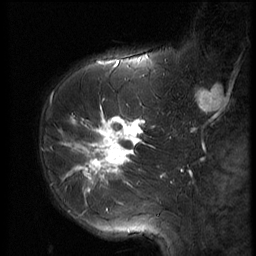
Breast MRI (dynamic contrast-enhanced), one sagittal slice; position 21 of 56 along the scan axis; 3 images stored at this slice position (order not interpretable as contrast timing); 1.5 T; TE 4.2 ms, TR 9 ms; 2.5 mm slice thickness; 256 × 256 image matrix. Patient: female, 61 years. Case-level facts recorded for this patient, not image findings: setting: breast cancer imaged before/during neoadjuvant chemotherapy; receptor status: HR-positive, HER2-negative.
Structures marked on this image (semi-automatic segmentation, software-assisted and operator-edited):
- analysis volume of interest (the breast-tissue region the enhancement analysis was run in; not a lesion): bounding box (x1, y1, x2, y2) in pixels: (47, 89, 153, 191)
- tumour enhancement mask (voxels above the 140 % enhancement threshold inside the analysis volume of interest): (61, 116, 144, 191)